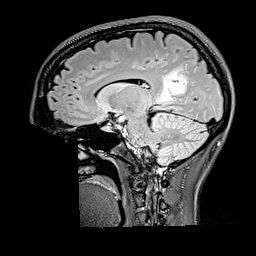
Brain MRI from a brain-tumour surgery series, one sagittal slice. Slice 97 of 176 in the series (ordered by position). T2 FLAIR. 1 mm slice thickness. 256 × 256 image matrix, field of view 256 × 256 mm. Case-level facts recorded for this patient, not image findings: histopathology: Oligodendroglioma; WHO grade: 2; IDH mutation: yes.
Annotated regions visible in this slice (manually delineated by an expert):
- tumour: bounding box [x1, y1, x2, y2] px = [160, 67, 188, 104]